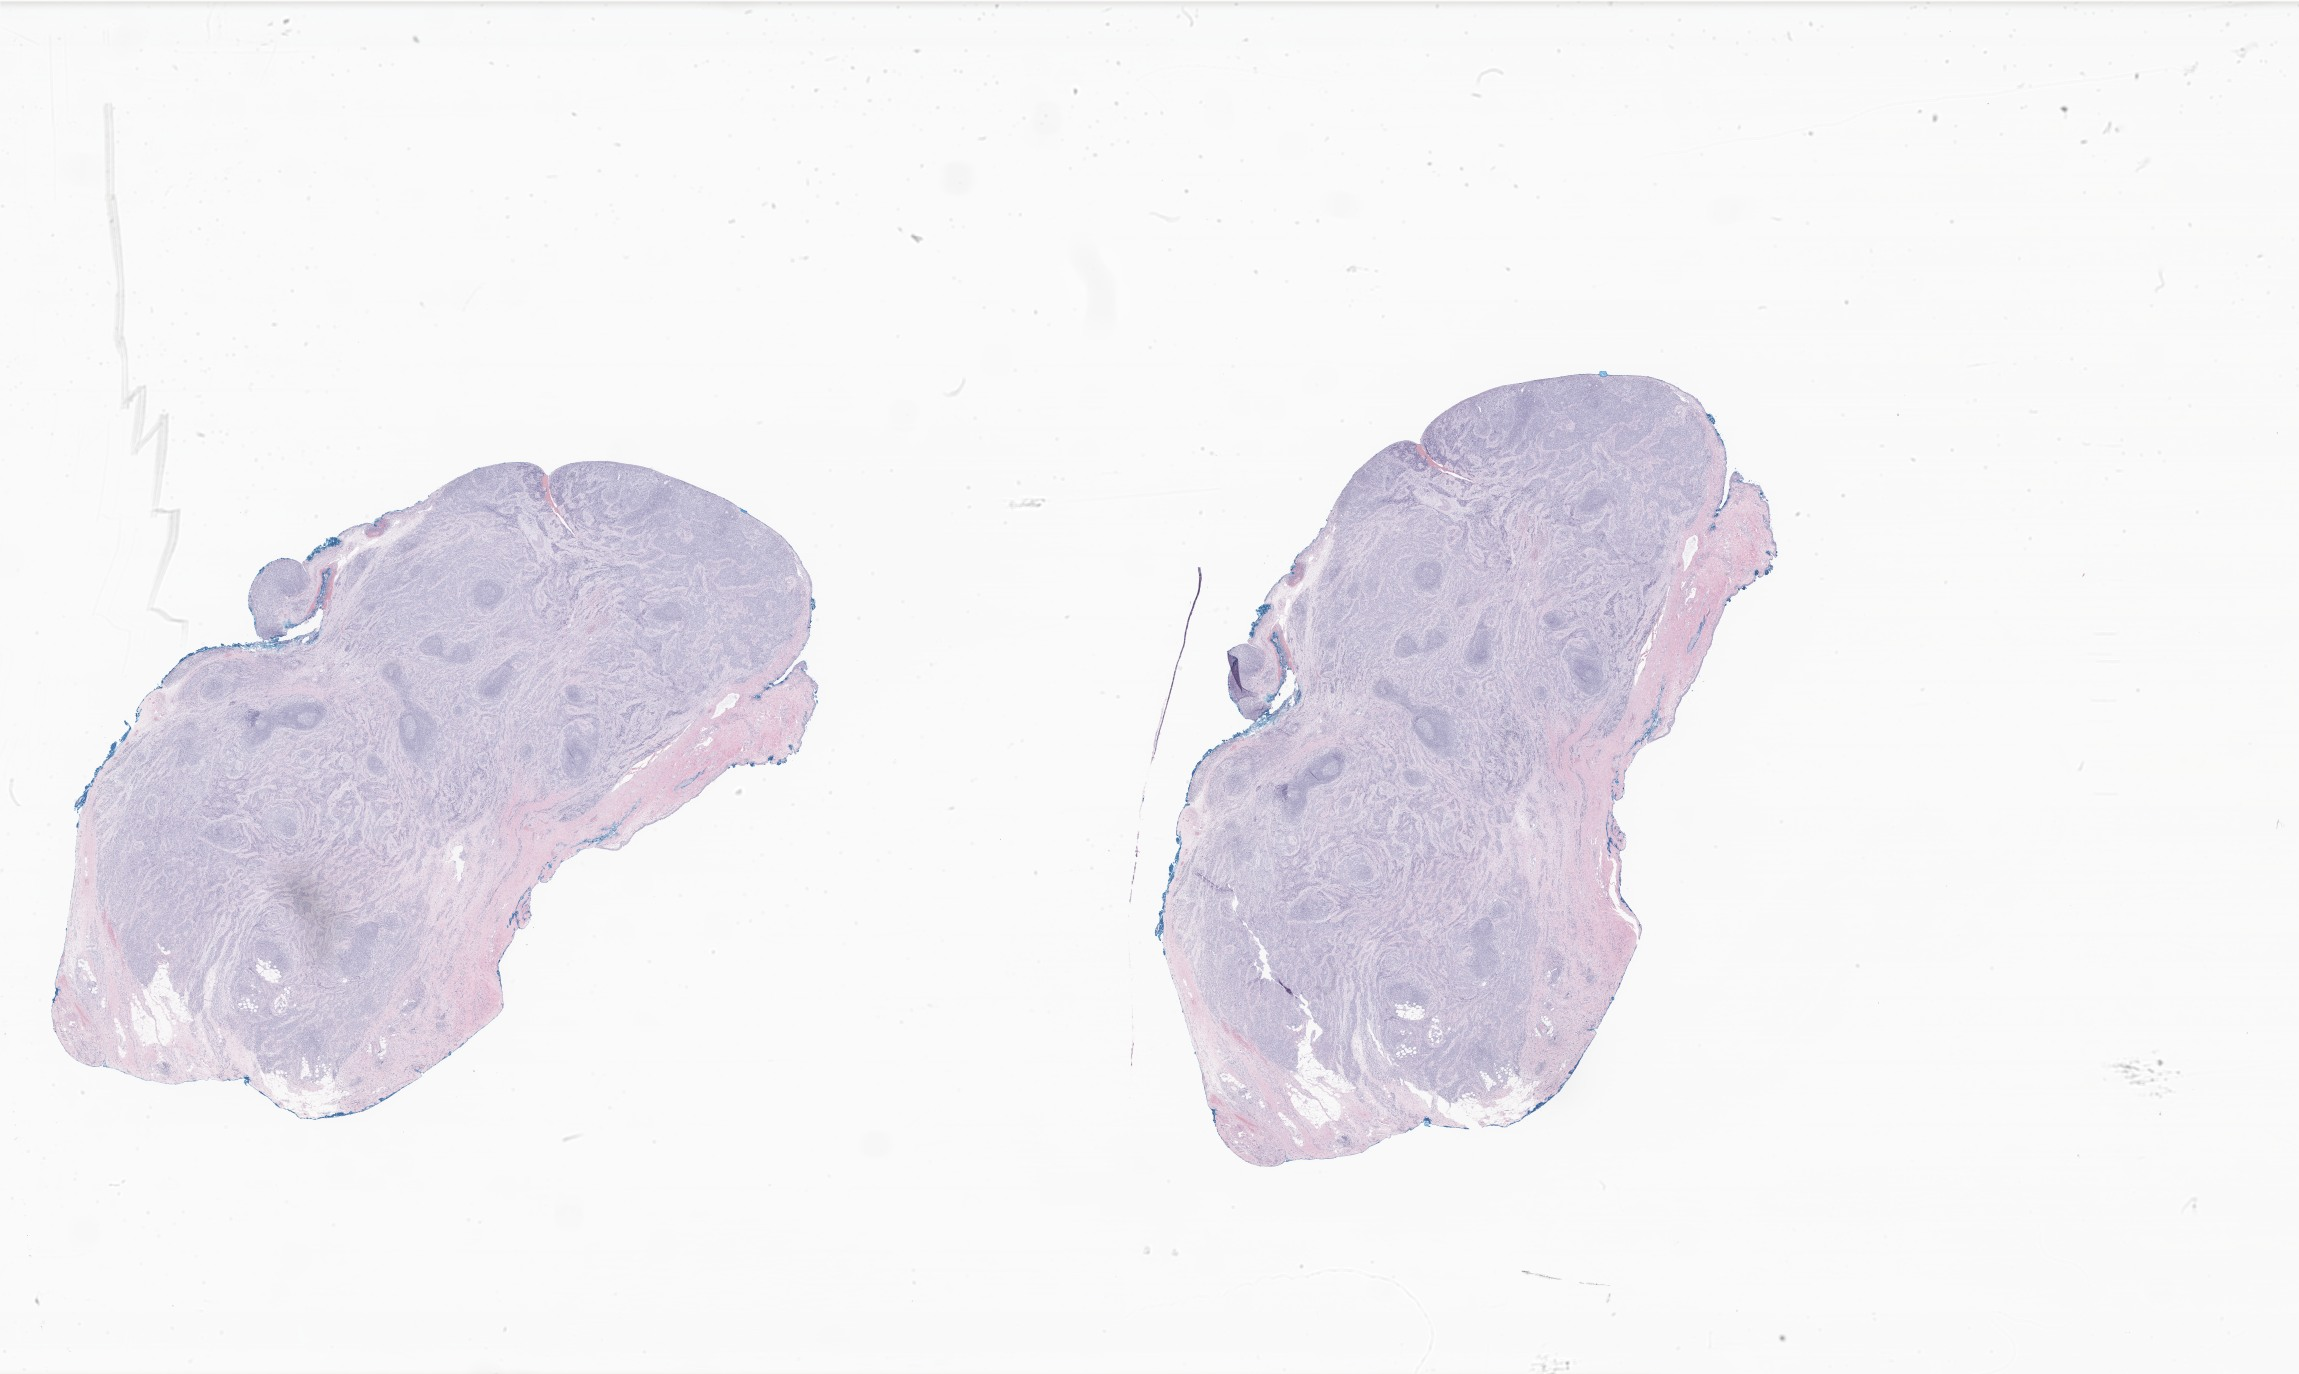
Whole-slide image, haematoxylin and eosin stain of tumor tissue from the orbit — whole scanned area (about 38.8 x 23.2 mm) shown as a low-resolution overview, FFPE section. Patient male; age 62 months (5 years 2 months).
* diagnosis: Alveolar rhabdomyosarcoma